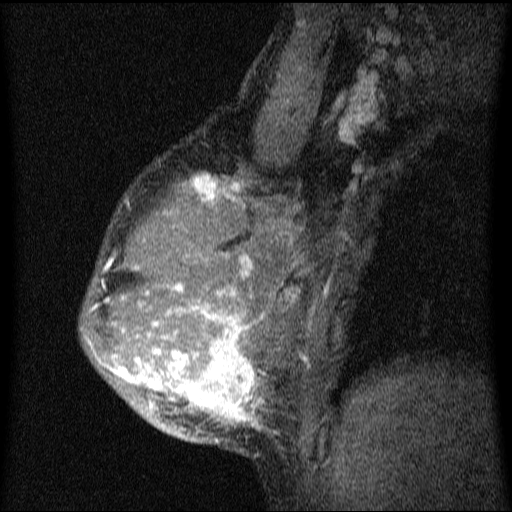
Breast MRI (dynamic contrast-enhanced), one sagittal slice. Slice 46 of 64 in the series (ordered by position). Dynamic contrast-enhanced series, image 2 of 4 at this slice position (ordered by acquisition). 1.5 T. TE 4.2 ms, TR 9.1 ms. 2 mm slice thickness. 512 × 512 image matrix, field of view 180 × 180 mm. Female patient, age 33 years.
Annotated regions visible in this slice (semi-automatically segmented with operator editing):
- analysis volume of interest (the breast-tissue region the enhancement analysis was run in; not a lesion): box from (x=80, y=151) to (x=331, y=455) px
- tumour enhancement mask (voxels above the 70 % enhancement threshold inside the analysis volume of interest): (x=86, y=174)–(x=306, y=444)